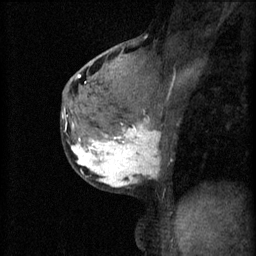
Breast MRI (dynamic contrast-enhanced), one sagittal slice. Position 34 of 60 along the scan axis. 3 images stored at this slice position (order not interpretable as contrast timing). 1.5 T. TE 4.2 ms, TR 11 ms. 2 mm slice thickness. 256 × 256 image matrix, field of view 180 × 180 mm. Female patient, age 37 years.
Structures marked on this image (semi-automatically segmented with operator editing):
- analysis volume of interest (the breast-tissue region the enhancement analysis was run in; not a lesion): bounding box (x1, y1, x2, y2) in pixels: (68, 118, 170, 191)
- tumour enhancement mask (voxels above the 70 % enhancement threshold inside the analysis volume of interest): (71, 118, 160, 187)